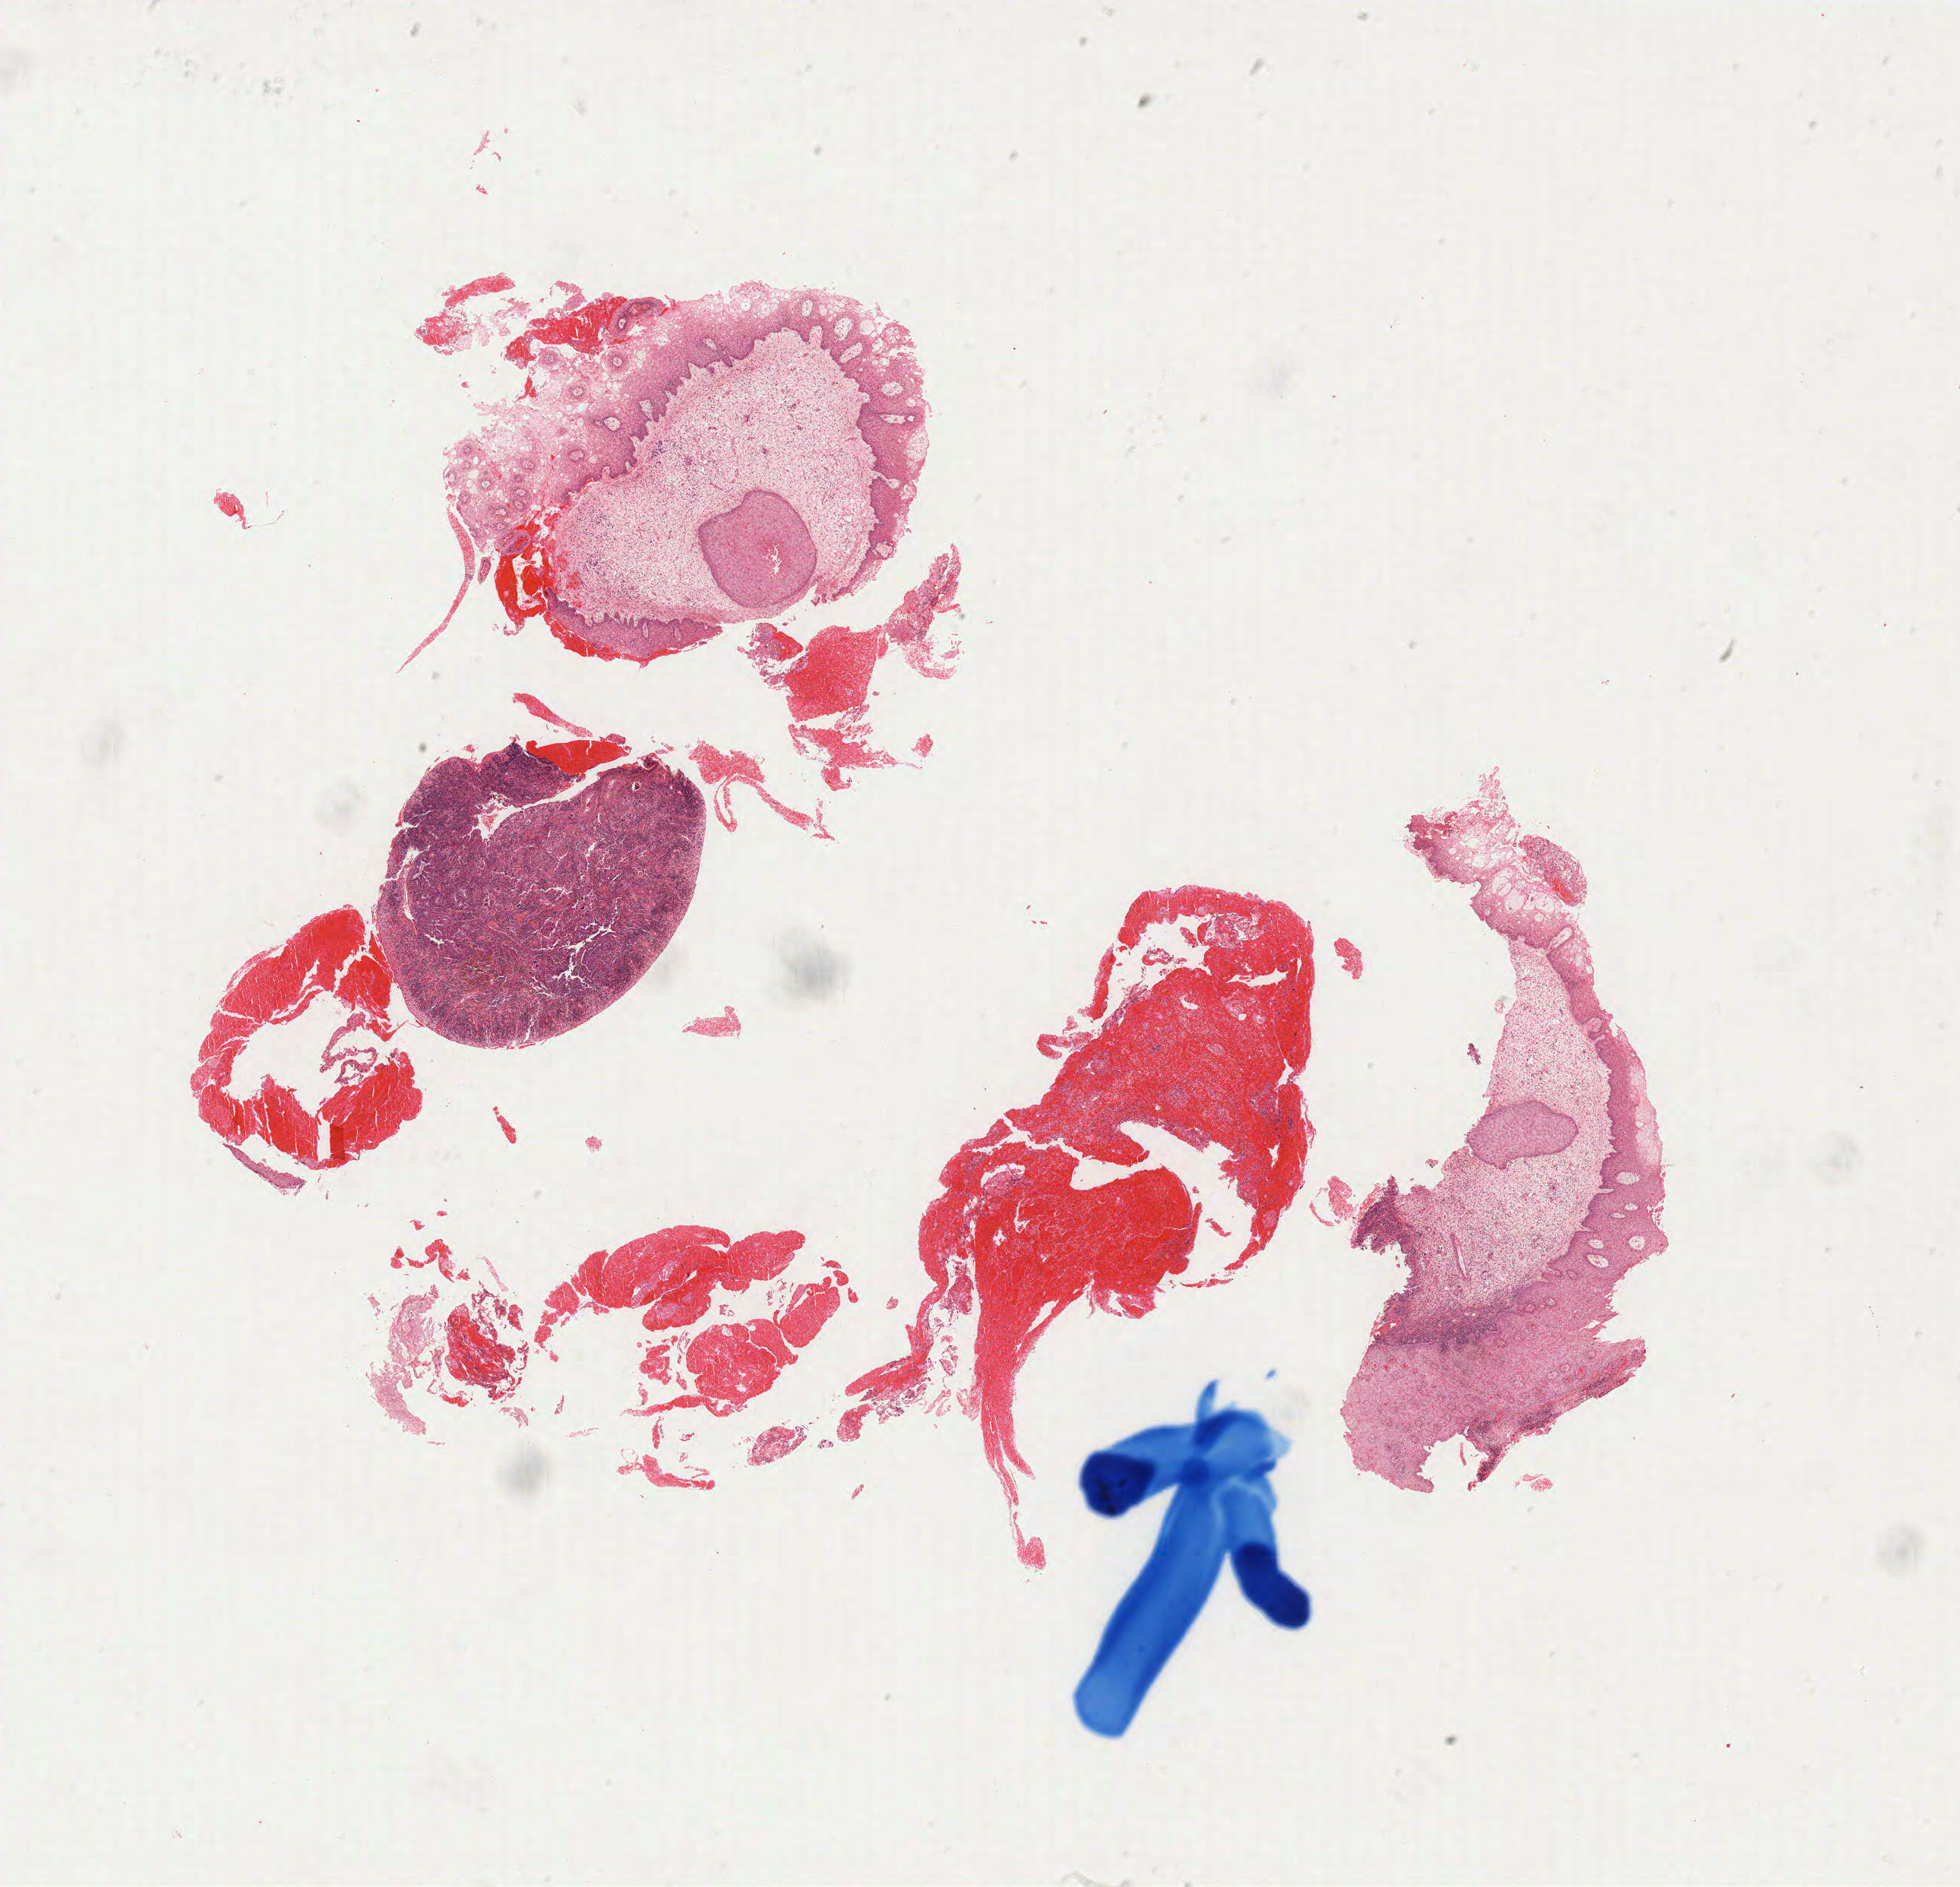
H&E whole-slide image — a low-resolution overview of the entire scanned area, about 20.6 x 19.9 mm (slide scanned at 40x), formalin-fixed paraffin-embedded (FFPE) diagnostic section, sample: primary tumour, cervix. Female, age 26 years at initial diagnosis. Histologic grade: G3 (poorly differentiated).
- diagnosis: Squamous cell carcinoma, NOS
- FIGO stage: IB2